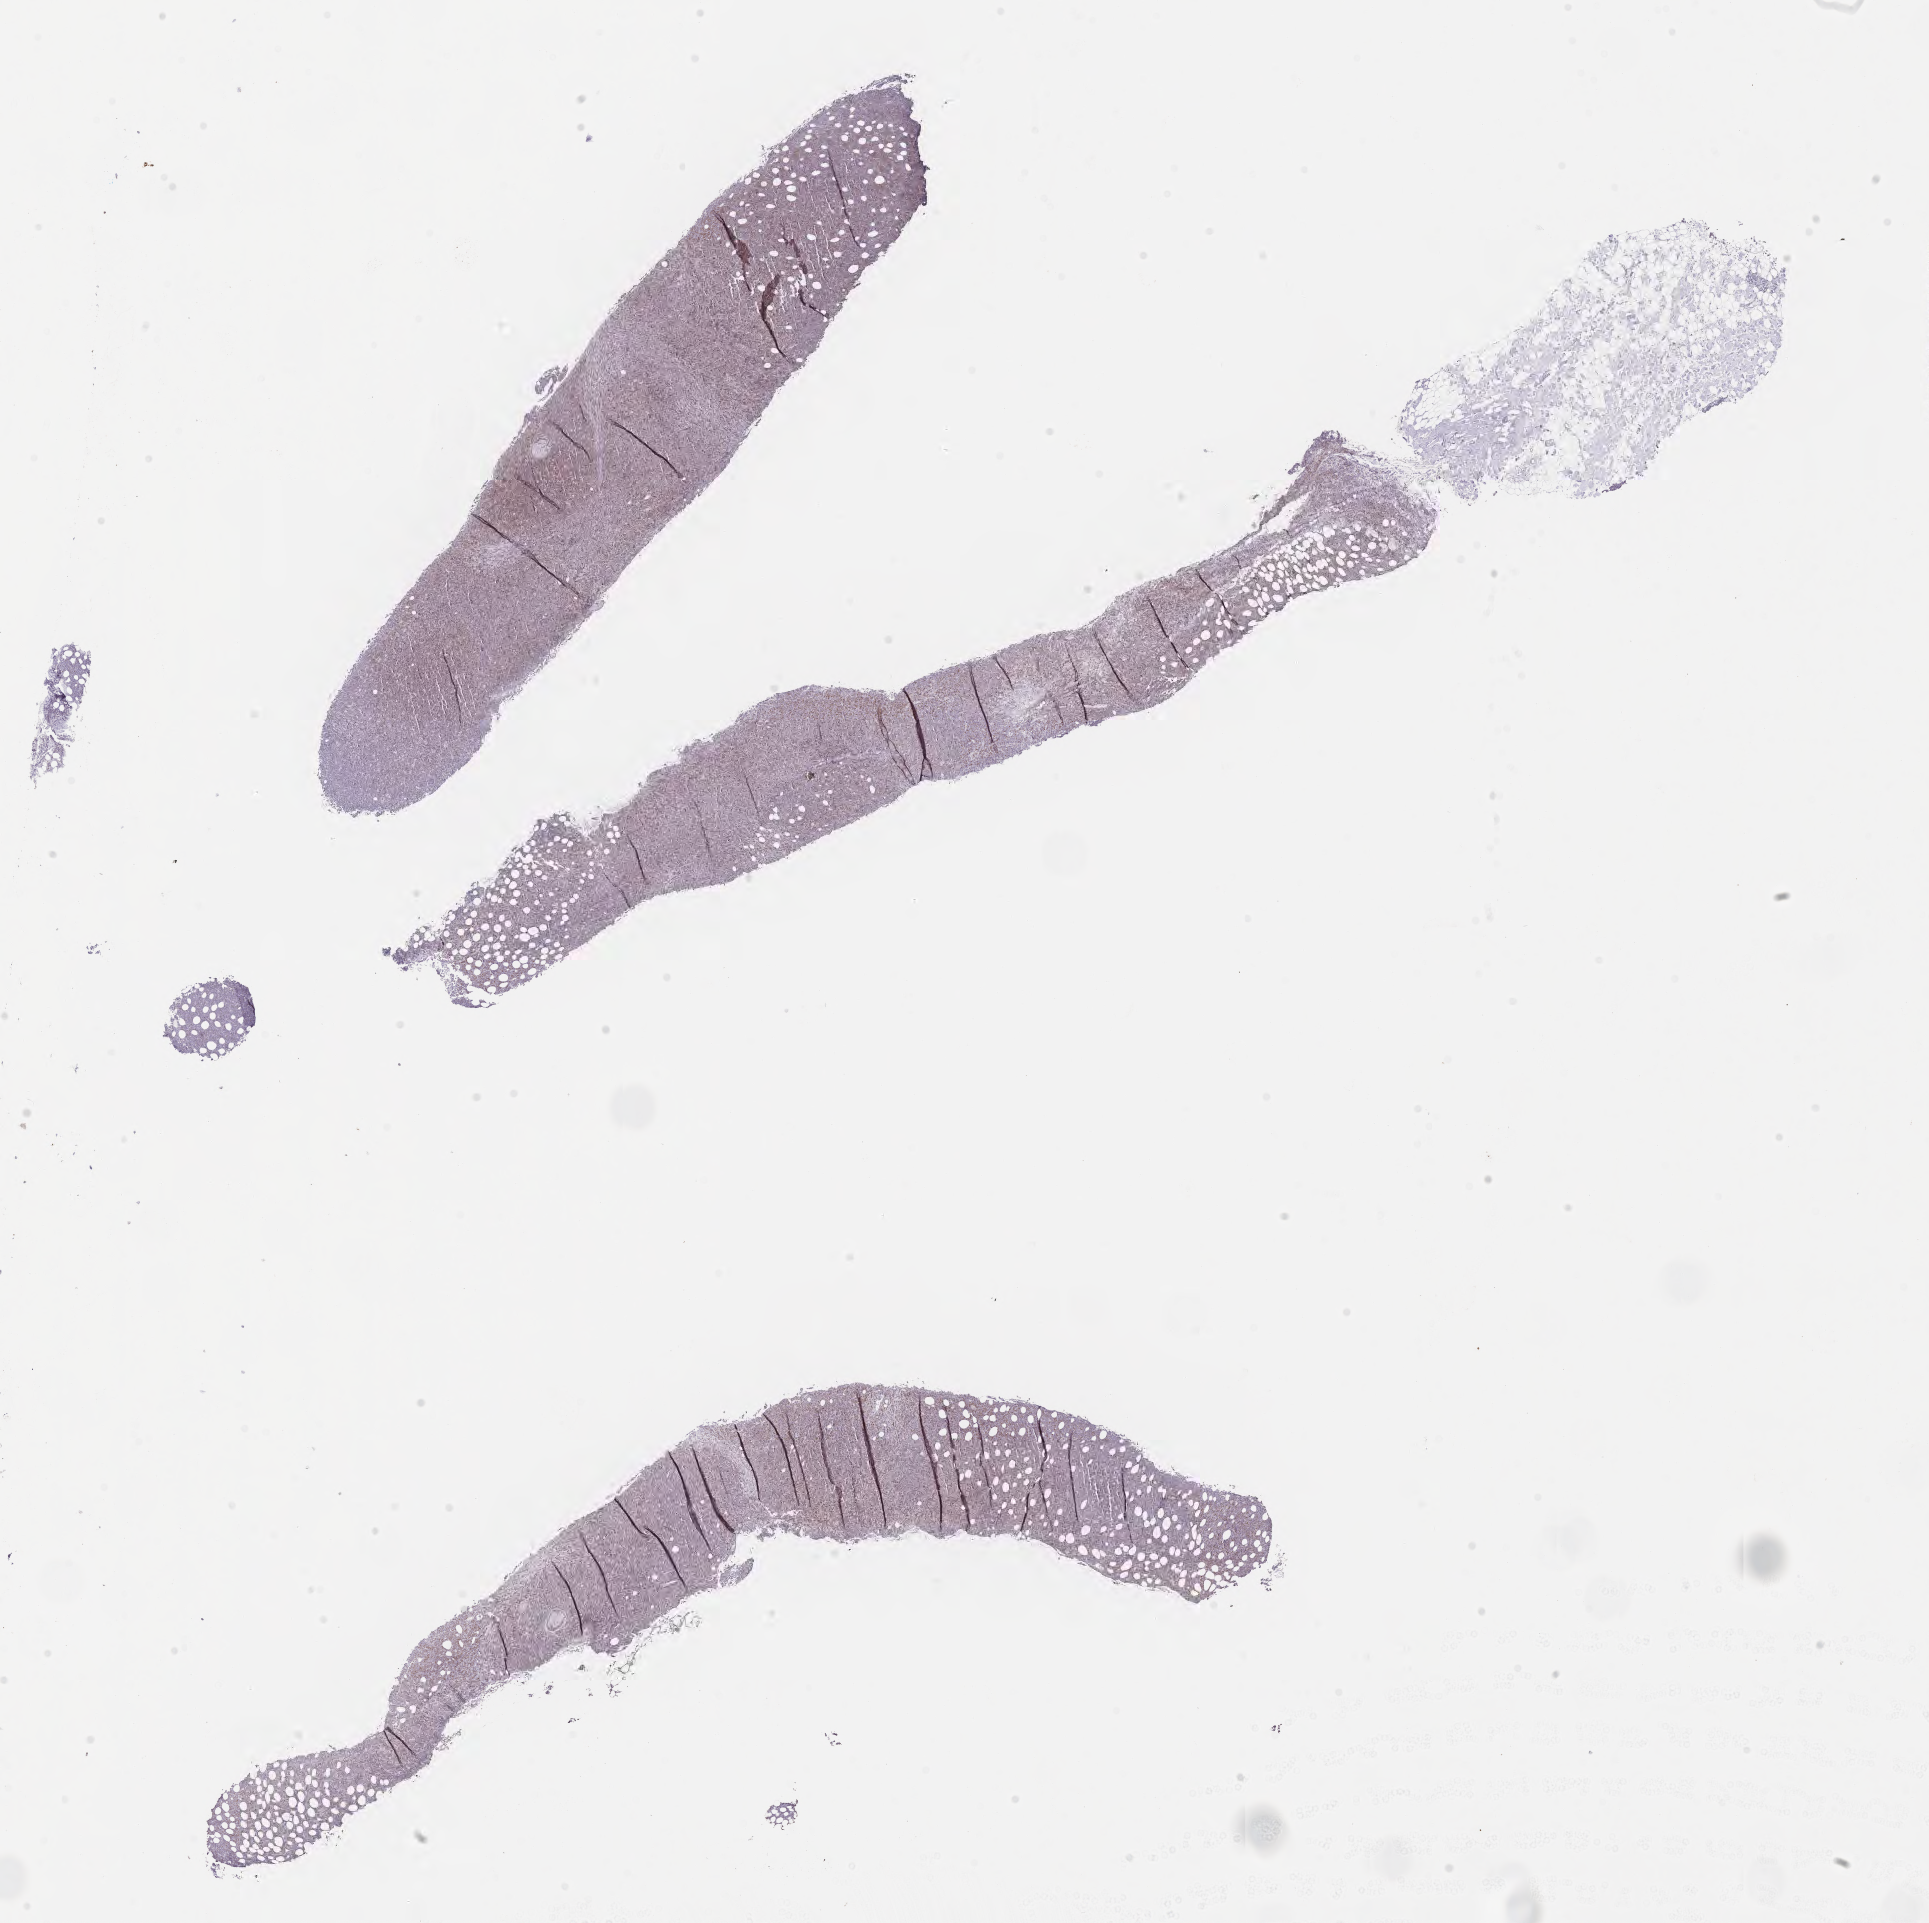
Immunohistochemistry (IHC) whole-slide image stained for BCL6, whole scanned area (about 15.6 x 15.5 mm) shown as a low-resolution overview. Tumor tissue. Female patient, age 43 years.
Histologic diagnosis: Burkitt lymphoma, NOS.